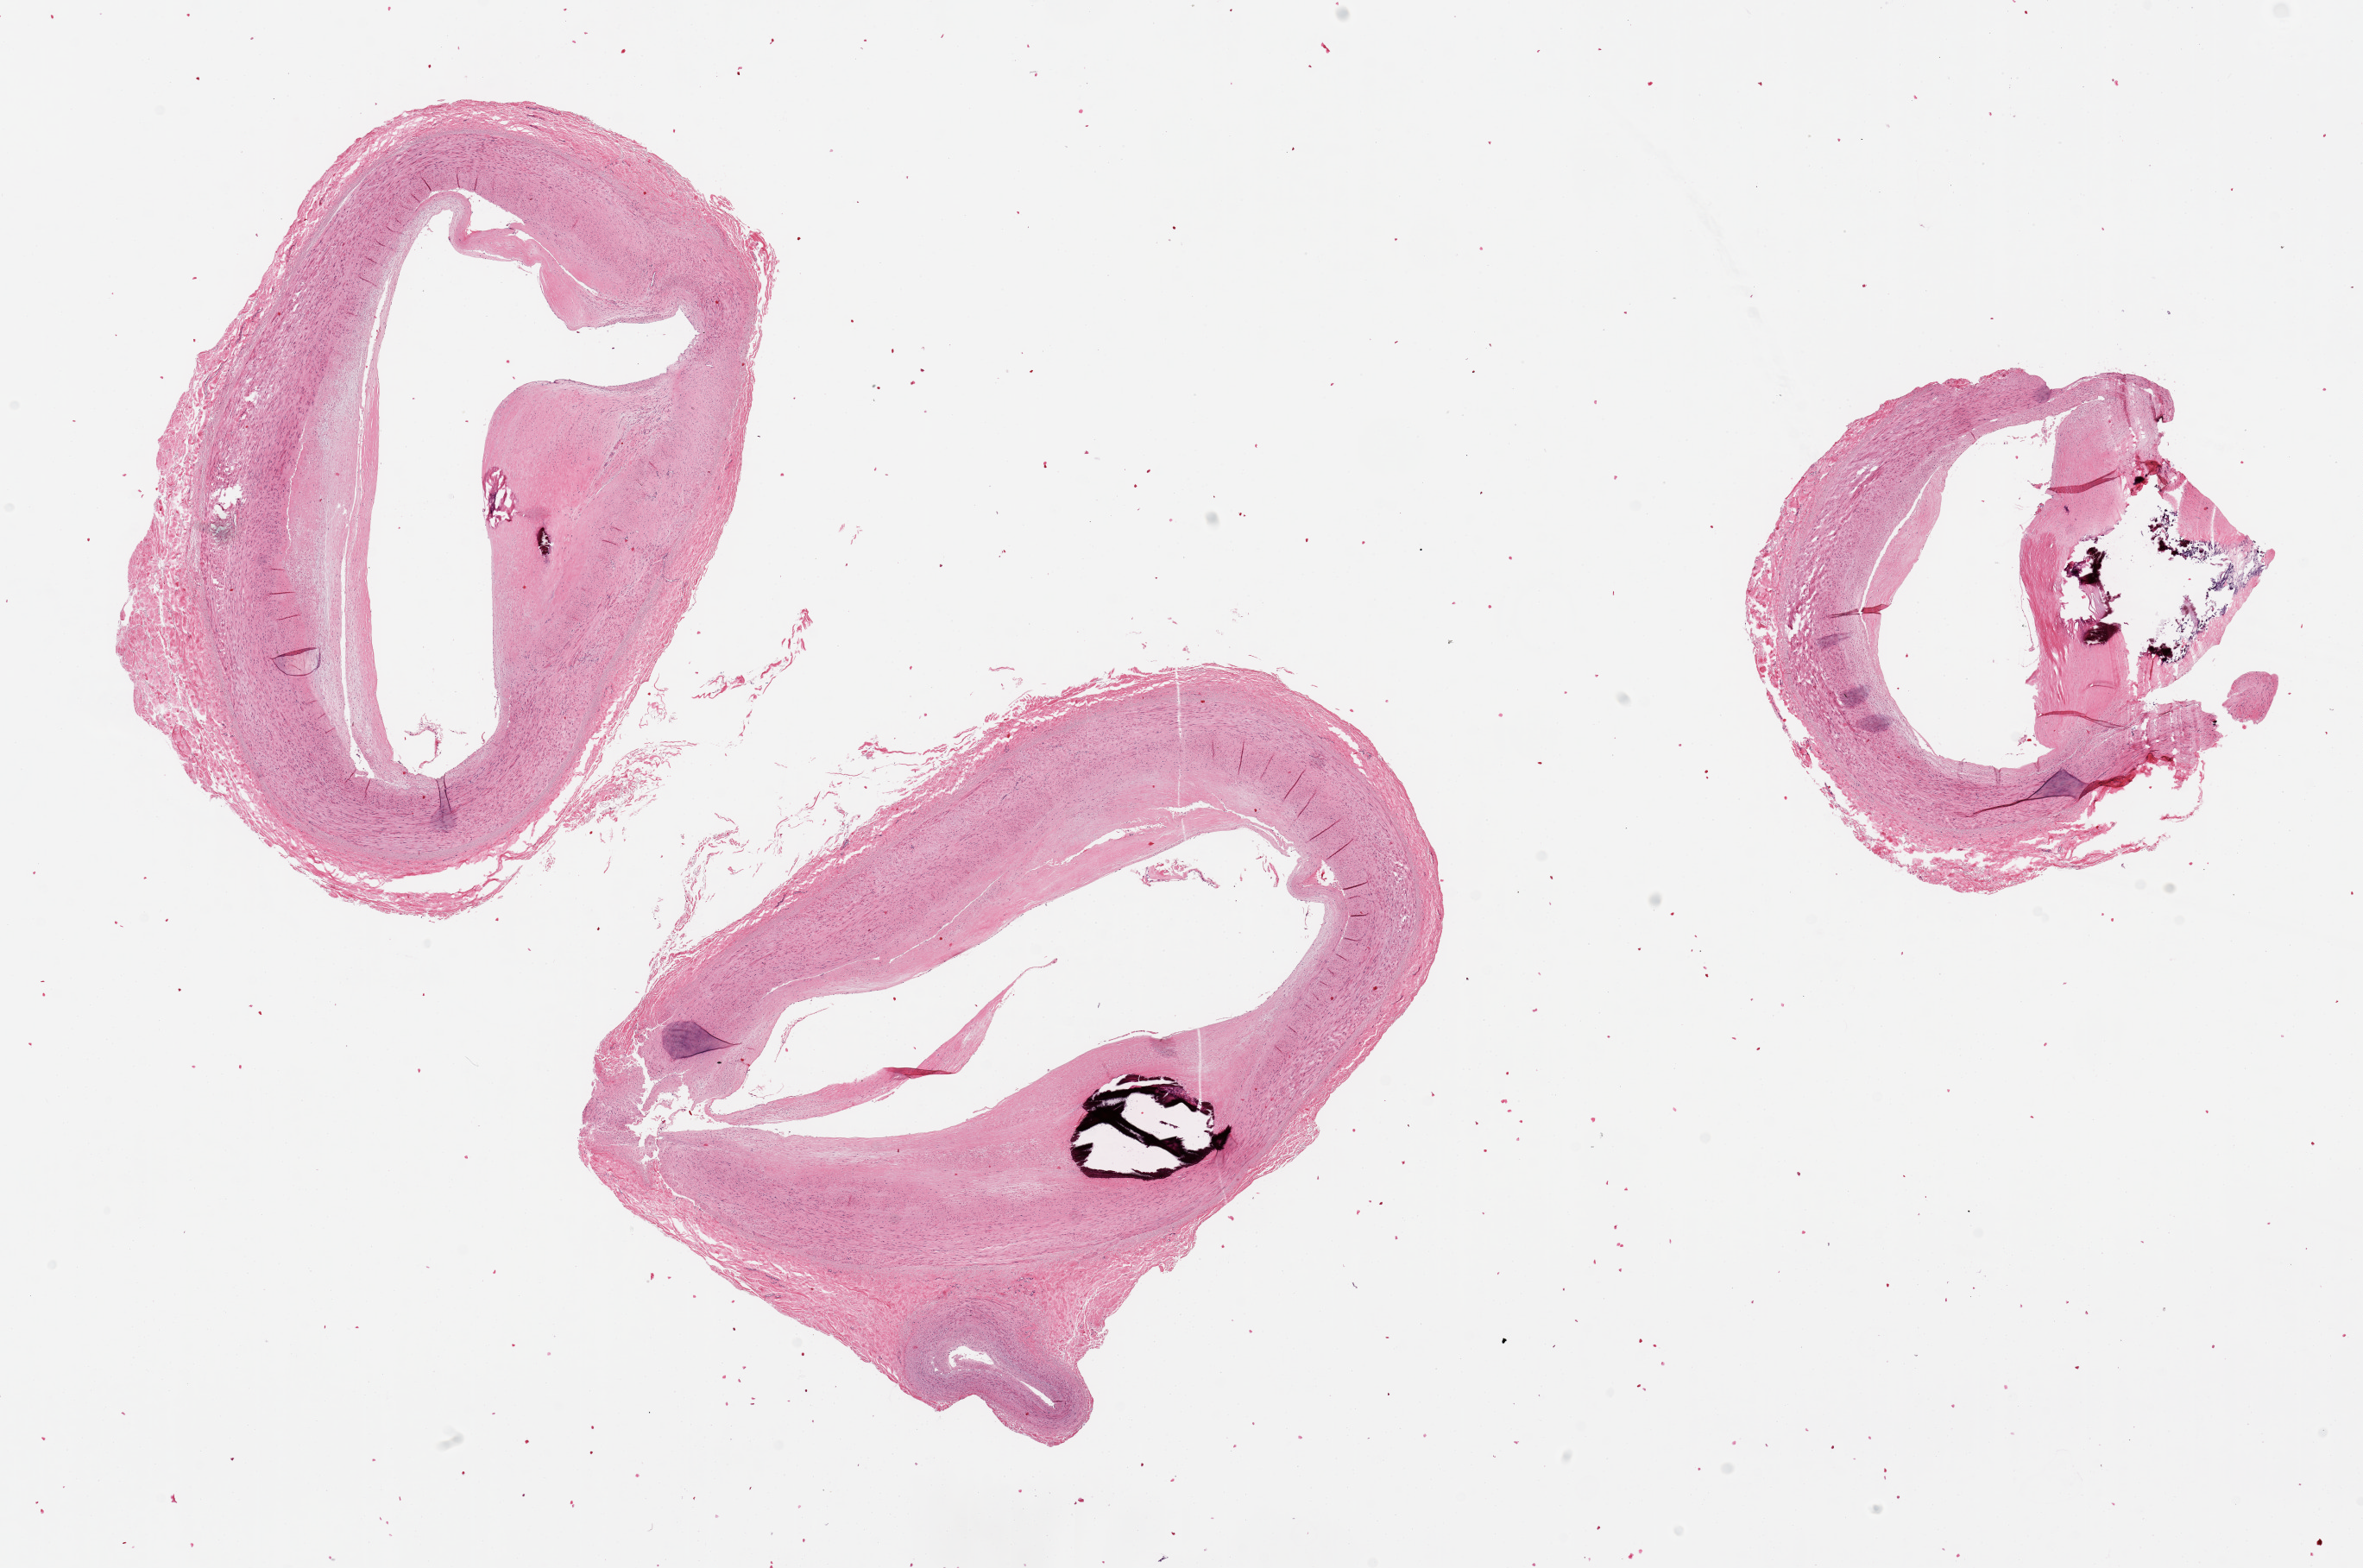
Whole-slide image, H&E stain, whole scanned area (about 21.7 x 14.4 mm, acquisition: 20x scan) shown as a low-resolution overview; PAXgene-fixed, paraffin-embedded tissue; target tissue: tibial artery; donor tissue sample. Male donor.
* reviewer comment on this tissue sample: 3 pieces, focally calcified partially (~40-50%)occlusive atherosis